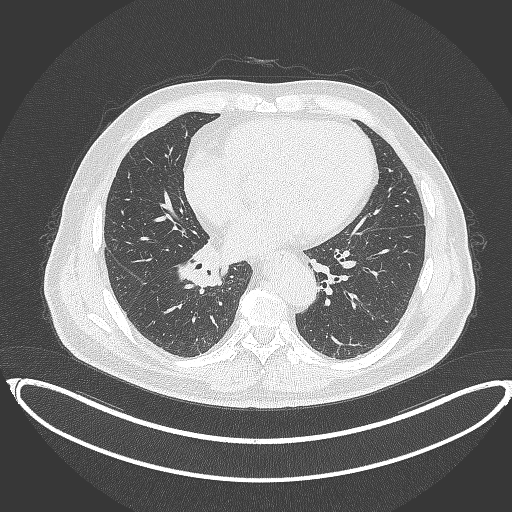
Chest CT, one axial slice; slice 172 of 387 in the series (ordered by position); reconstruction kernel B70f; 120 kVp; lung window (W 1500 / L -600 HU); 1 mm slice thickness; 512 × 512 image matrix, field of view 448 × 448 mm. Patient: male, 61 years. From the clinical record (not read from this slice): clinical TNM (as recorded): T1b N1 M0.
Structures marked on this image (rectangle marked by the reading radiologist):
- lung tumour (recorded histology: squamous cell carcinoma): bounding box [x1, y1, x2, y2] px = [176, 240, 224, 293]